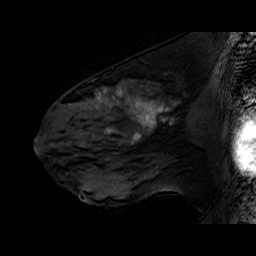
Breast MRI (dynamic contrast-enhanced), one sagittal slice; position 32 of 60 along the scan axis; dynamic contrast-enhanced series, time point 2 of 6 at this slice position (early post-contrast); 1.5 T; TE 6.4 ms, TR 32.9 ms; 4 mm slice thickness; 256 × 256 image matrix, field of view 200 × 200 mm. Female patient. From the clinical record (not read from this slice): setting: breast cancer imaged before/during neoadjuvant chemotherapy; receptor status: HER2-positive.
Structures marked on this image (semi-automatic segmentation, software-assisted and operator-edited):
- analysis volume of interest (the breast-tissue region the enhancement analysis was run in; not a lesion): bounding box [x1, y1, x2, y2] px = [51, 78, 196, 160]
- tumour enhancement mask (voxels above the 100 % enhancement threshold inside the analysis volume of interest): [95, 88, 155, 131]